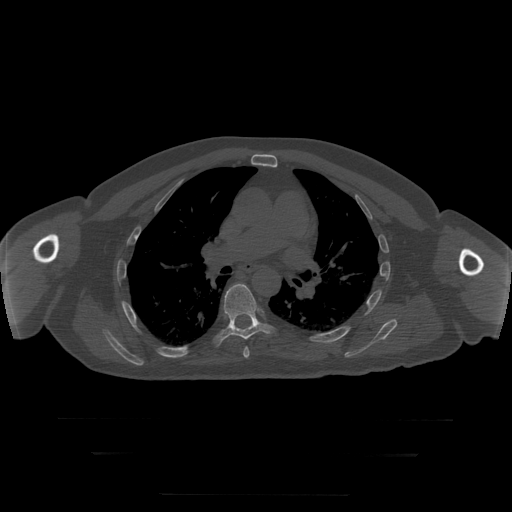
CT including the spine, one axial slice; slice 190 of 397 in the series (ordered by position); reconstruction kernel STANDARD; 120 kVp; bone window (W 1800 / L 400 HU); 512 × 512 image matrix, field of view 510 × 510 mm. Patient age 73 years. From the clinical record (not read from this slice): primary cancer: prostate.
Annotated regions visible in this slice (semi-automatic segmentation, software-assisted and operator-edited):
- T6 vertebra: bounding box [x1, y1, x2, y2] px = [244, 348, 250, 359]
- T7 vertebra: [213, 284, 276, 347]